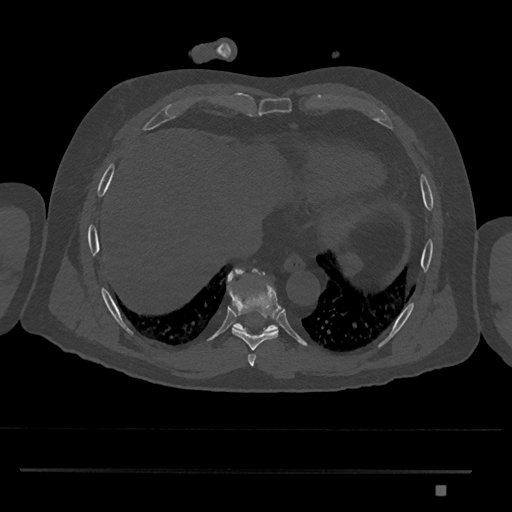
CT including the spine, one axial slice; position 1093 of 1134 along the scan axis; bone window (W 1800 / L 400 HU); 0.5 mm slice thickness; 512 × 512 image matrix, field of view 429 × 429 mm. Male patient, age 65 years. Case-level facts recorded for this patient, not image findings: primary cancer: prostate.
Annotated regions visible in this slice (semi-automatically segmented with operator editing):
- T8 vertebra: bounding box <232,269,281,350> (left, top, right, bottom; pixels)
- T9 vertebra: <227,268,278,333>